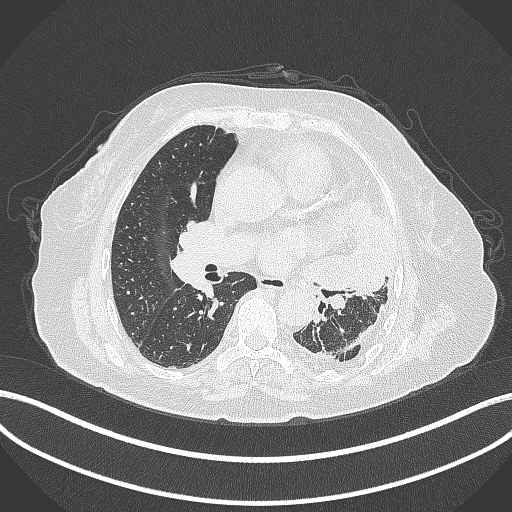
Chest CT, one axial slice. Slice 192 of 399 in the series (ordered by position). Reconstruction kernel B70f. 120 kVp. Lung window (W 1500 / L -600 HU). 1 mm slice thickness. 512 × 512 image matrix. Patient: female, 75 years. From the clinical record (not read from this slice): clinical TNM (as recorded): T3 N3 M1.
Outlined on this slice (bounding box drawn by a radiologist):
- lung tumour (recorded histology: adenocarcinoma): bounding box <312,201,401,296> (left, top, right, bottom; pixels)